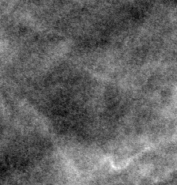
Region of interest cut from a scanned film mammogram (one marked finding); right breast; MLO view; BI-RADS breast density category 1 (scale 1–4).
Finding: calcifications, morphology fine linear branching; BI-RADS assessment category 2; benign without callback (not worked up further).